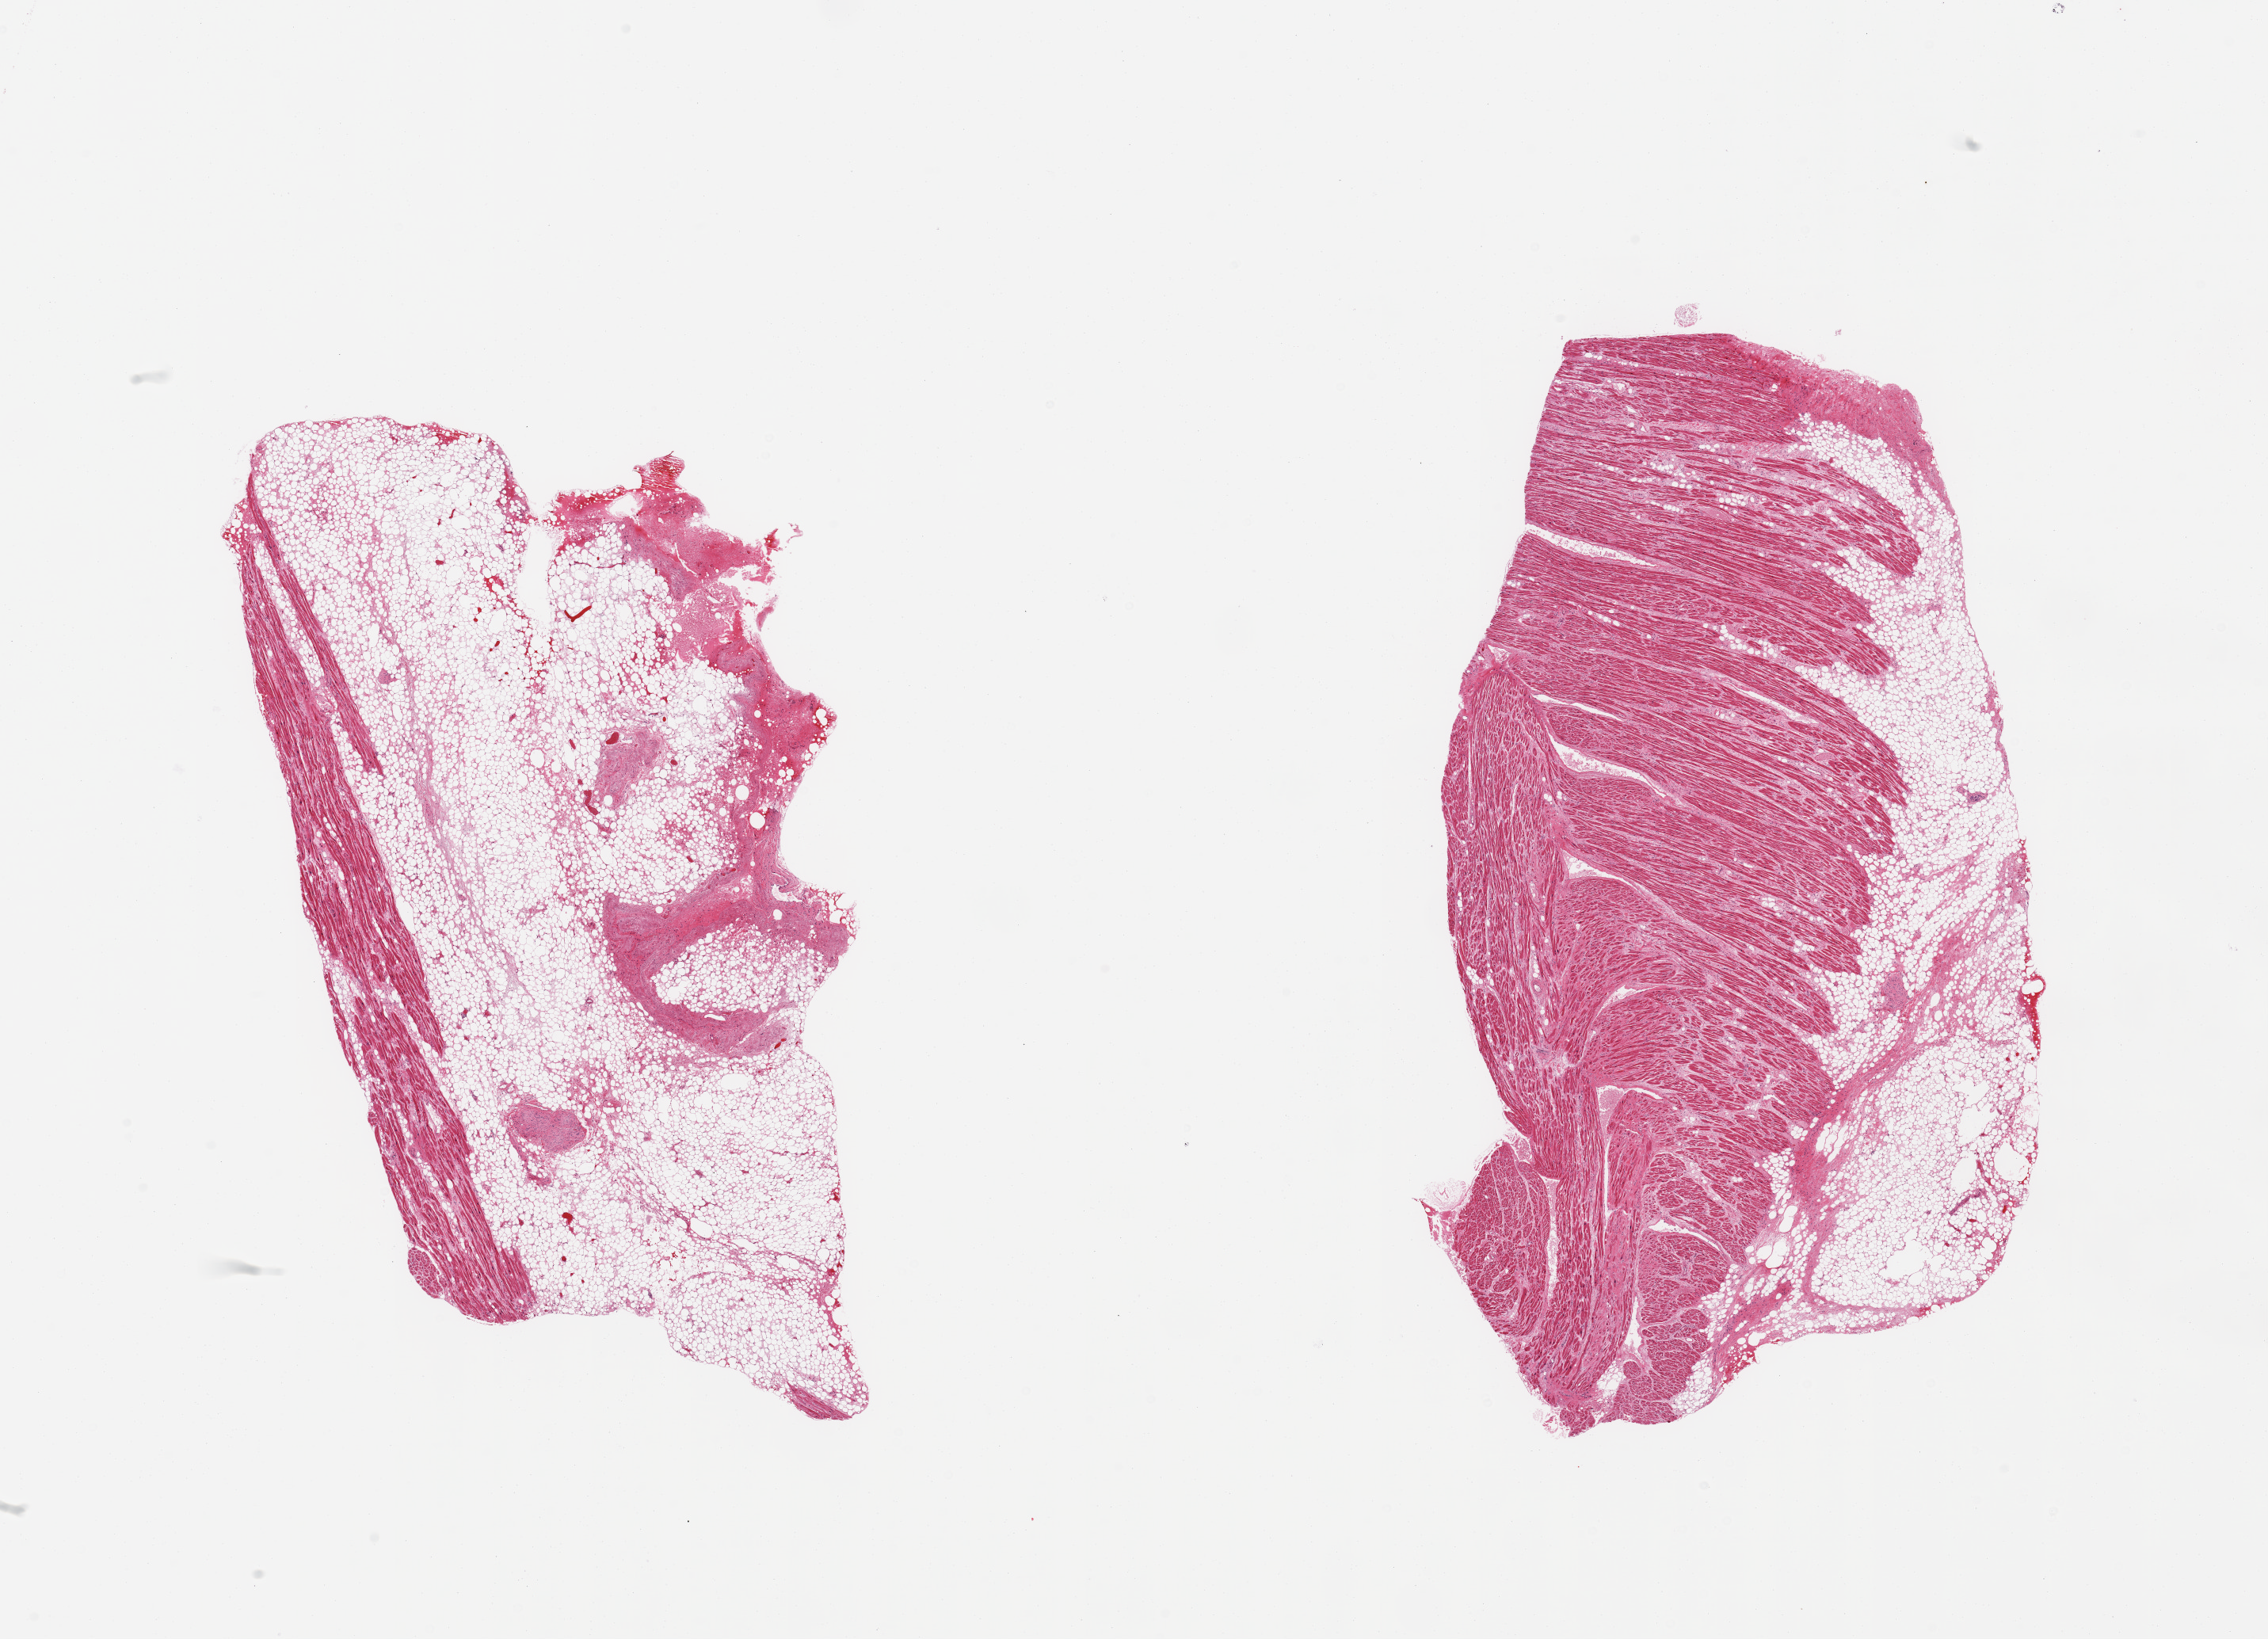
H&E whole-slide image — low-resolution overview of the scanned area, about 22.6 x 16.4 mm (from a 20x scan); PAXgene-fixed, paraffin-embedded tissue; section of auricular appendage (target tissue); tissue donor sample. Donor sex: male.
Reviewer comment on this tissue sample: 2 pieces, no abnormalities.